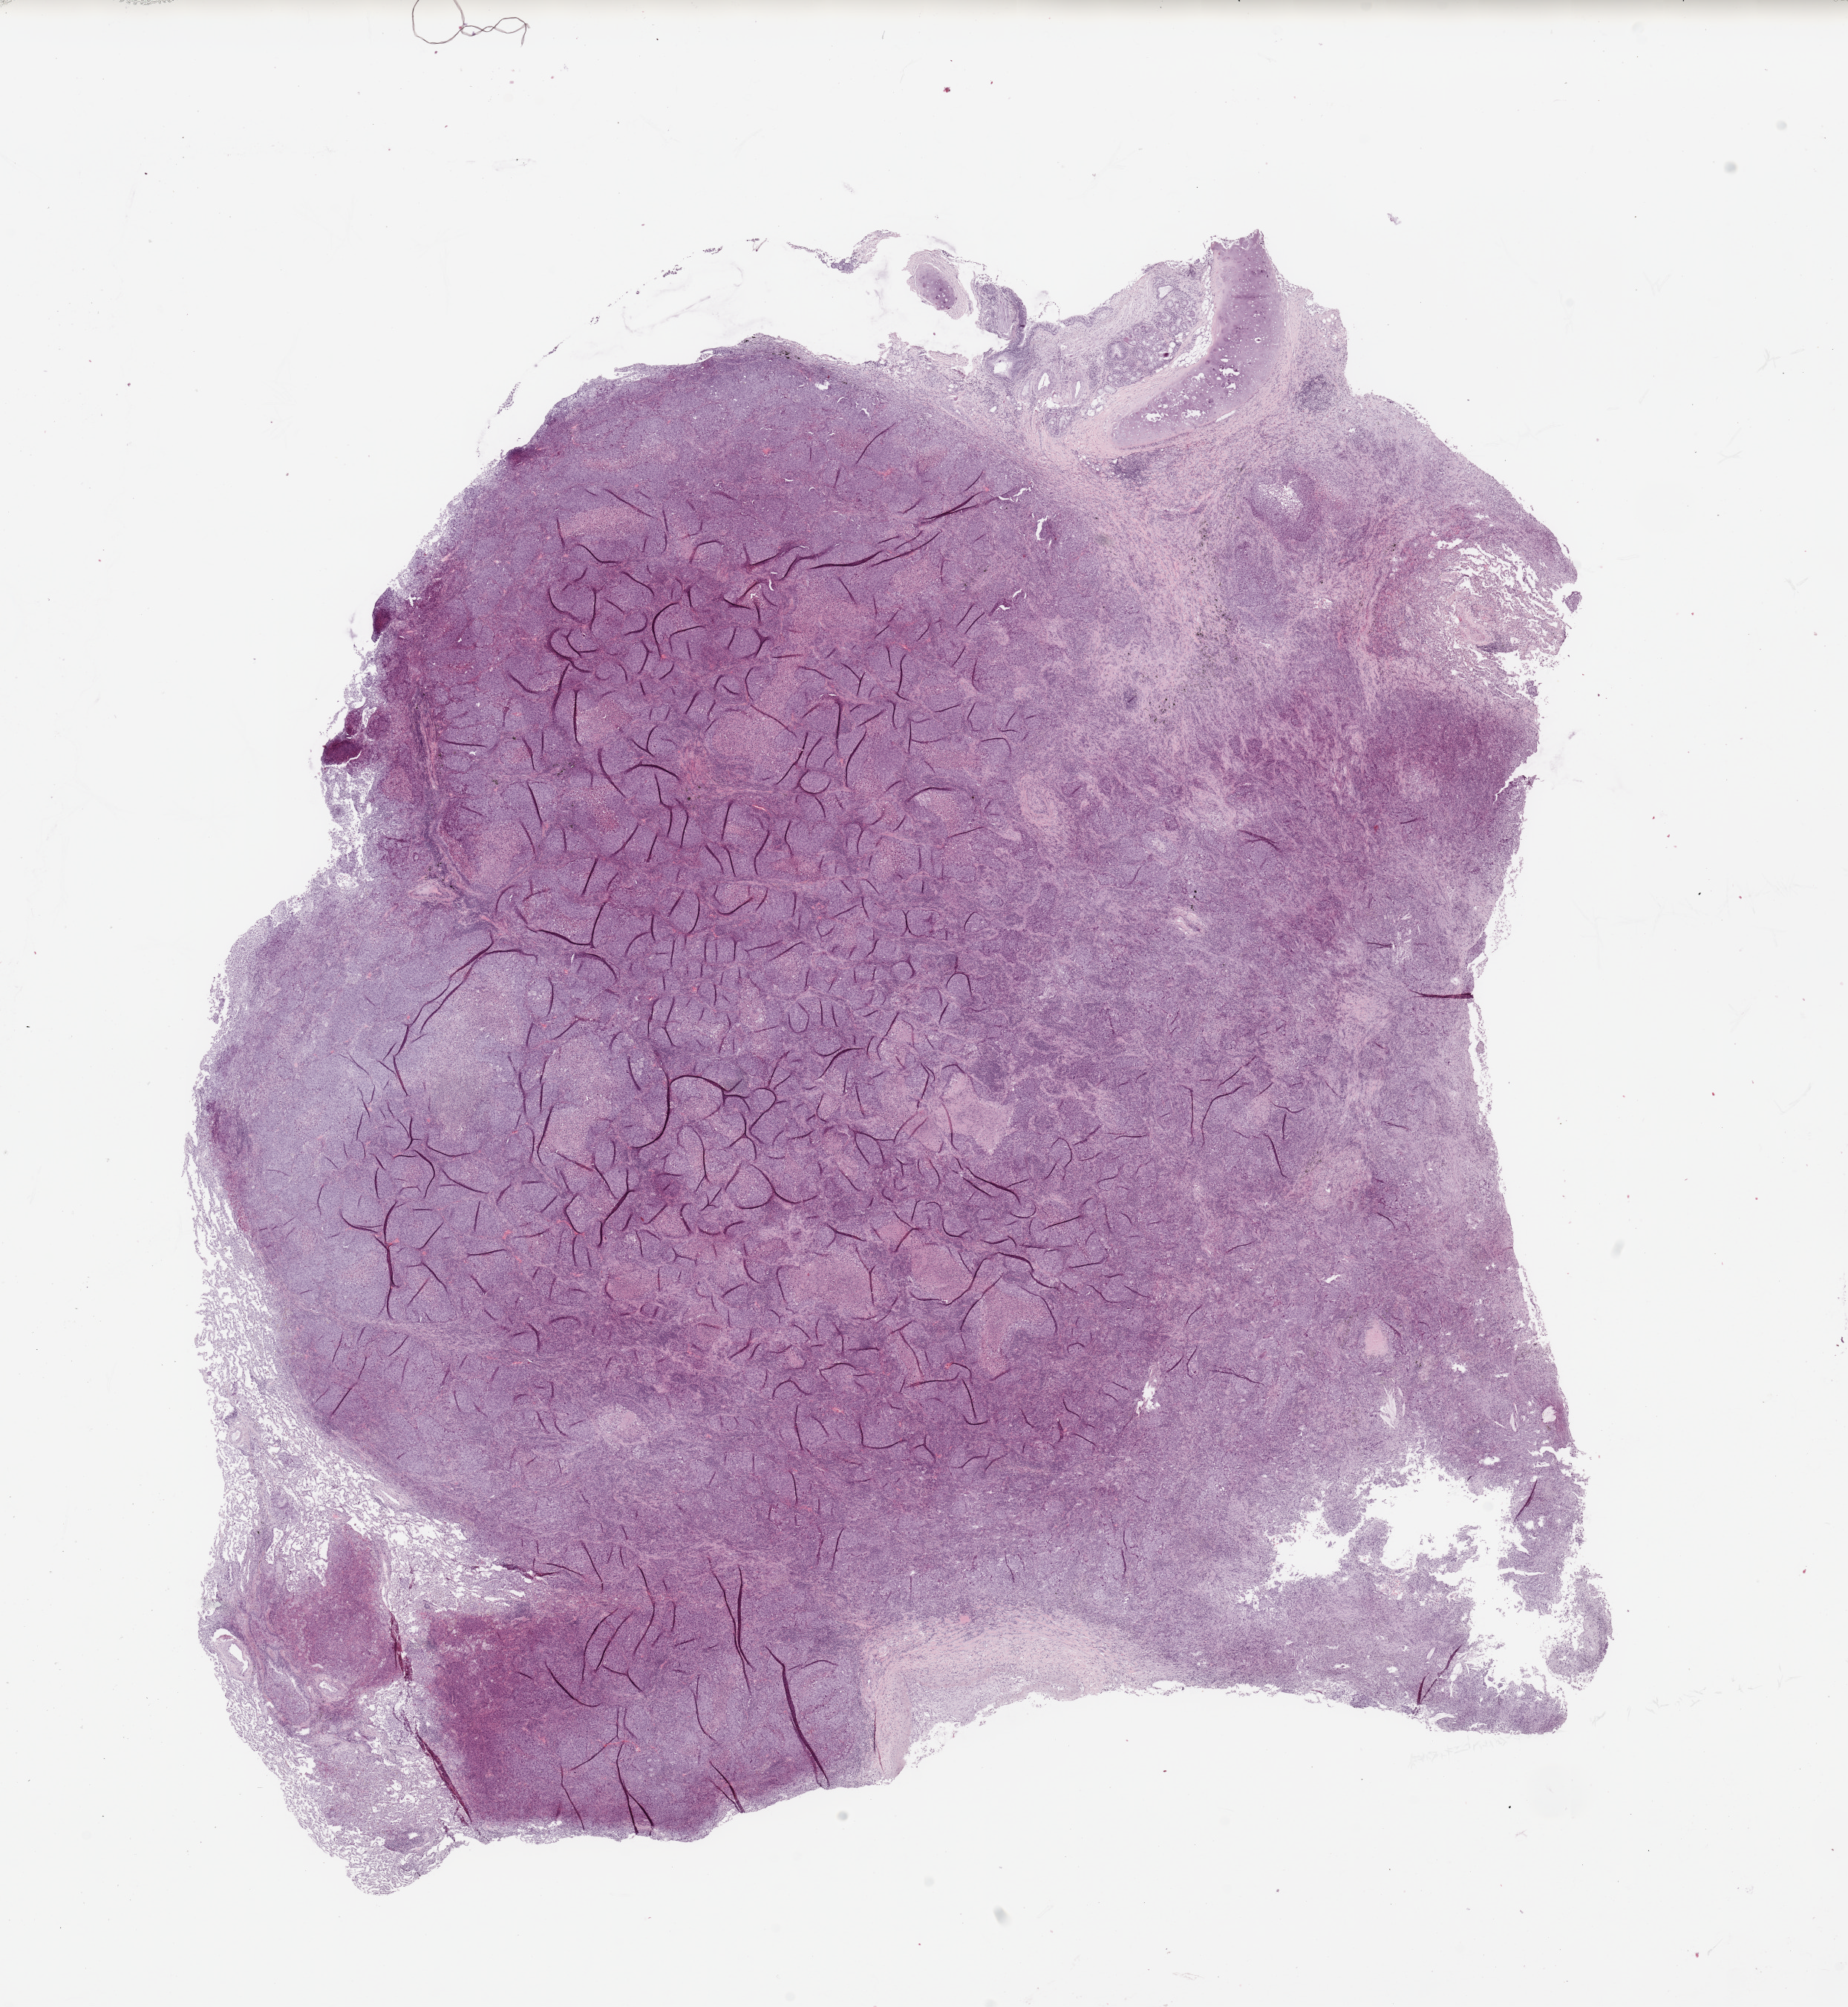
Whole-slide histology image, H&E-stained, a low-resolution overview of the entire scanned area, about 19.7 x 21.4 mm (from a 20x scan); lung, tumour tissue. Patient: male, age 61 years. Histologic grade: G2 (moderately differentiated).
Diagnosis: Squamous cell carcinoma, NOS. Primary tumour site (as recorded): right upper lobe.